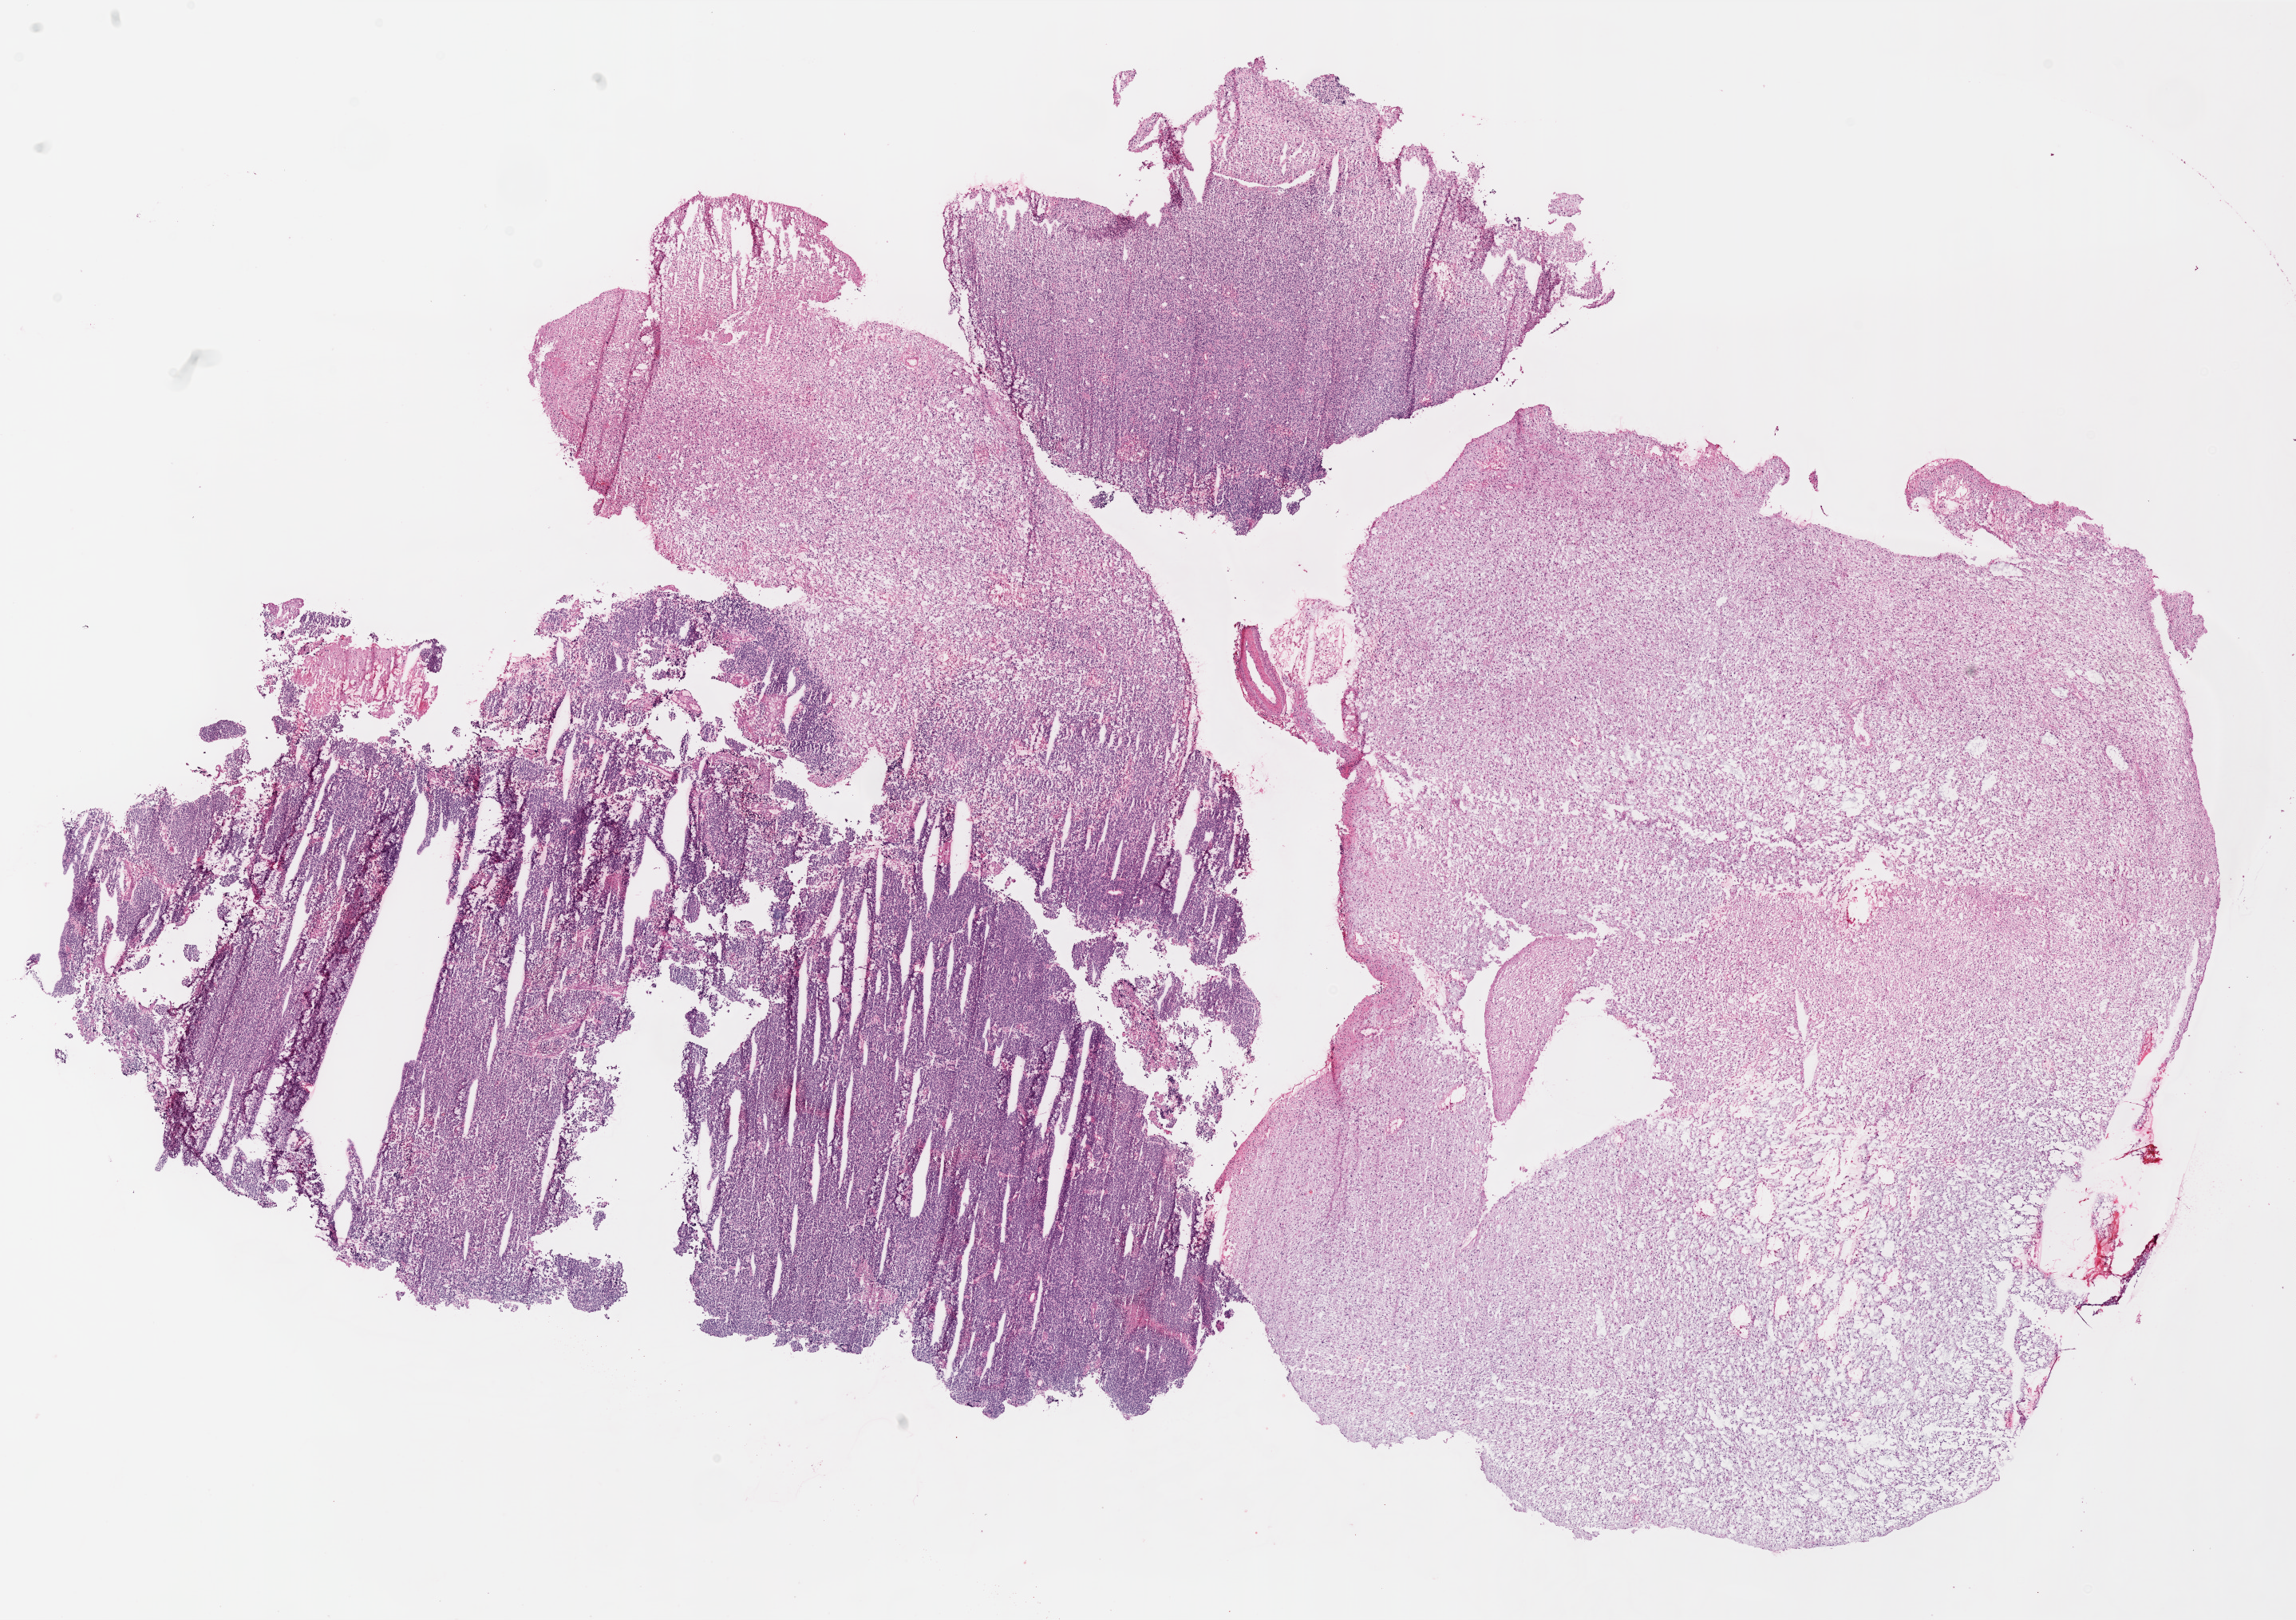
H&E-stained whole-slide image, a low-resolution overview of the entire scanned area, about 23.1 x 16.3 mm (slide scanned at 20x), frozen section from the top of the tissue portion, primary tumour sample from the brain. Female patient; age at initial diagnosis 29 years. Slide review estimates, as recorded: tumour cells 95%, tumour nuclei 100%, normal cells 0%, stromal cells 0%, necrosis 5%.
Pathologic diagnosis: Glioblastoma.